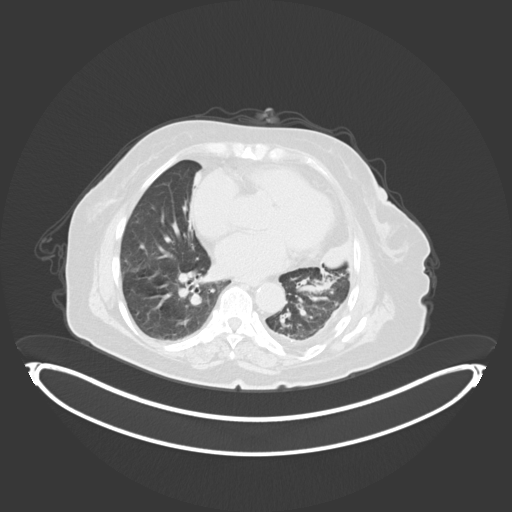
Chest CT, one axial slice; position 188 of 284 along the scan axis; reconstruction kernel B30f; 120 kVp; lung window (W 1500 / L -600 HU); 512 × 512 image matrix, field of view 500 × 500 mm. Patient: female, 75 years. From the clinical record (not read from this slice): clinical TNM (as recorded): T3 N3 M1.
Outlined on this slice (rectangle marked by the reading radiologist):
- lung tumour (recorded histology: adenocarcinoma): box from (x=315, y=236) to (x=354, y=274) px